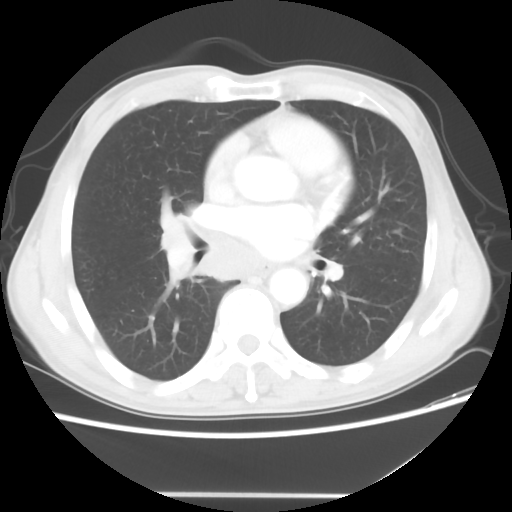
Chest CT, one axial slice; slice 26 of 56 in the series (ordered by position); lung window (W 1500 / L -600 HU); 5 mm slice thickness; 512 × 512 image matrix, field of view 344 × 344 mm. Patient: male, 65 years. From the clinical record (not read from this slice): clinical TNM (as recorded): T1c N3 M0.
Annotated regions visible in this slice (bounding box drawn by a radiologist):
- lung tumour (recorded histology: small cell carcinoma): bounding box [x1, y1, x2, y2] px = [157, 200, 261, 283]